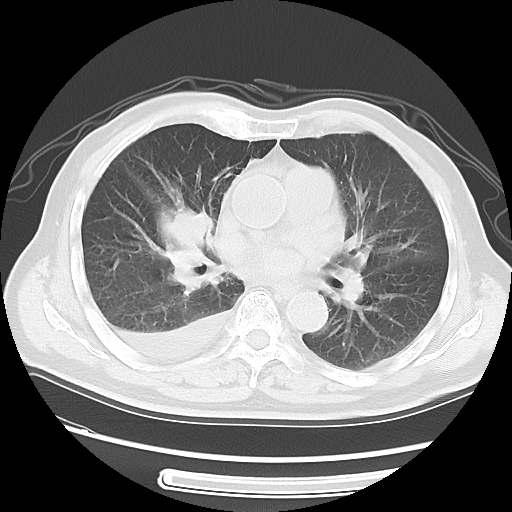
Chest CT, one axial slice. Slice 28 of 56 in the series (ordered by position). Reconstruction kernel LUNG. Lung window (W 1500 / L -600 HU). 5 mm slice thickness. 512 × 512 image matrix, field of view 360 × 360 mm. Male patient, age 77 years. Case-level facts recorded for this patient, not image findings: clinical TNM (as recorded): T3 N3 M1b.
Annotated regions visible in this slice (bounding box drawn by a radiologist):
- lung tumour (recorded histology: small cell carcinoma): bounding box (x1, y1, x2, y2) in pixels: (163, 201, 221, 297)